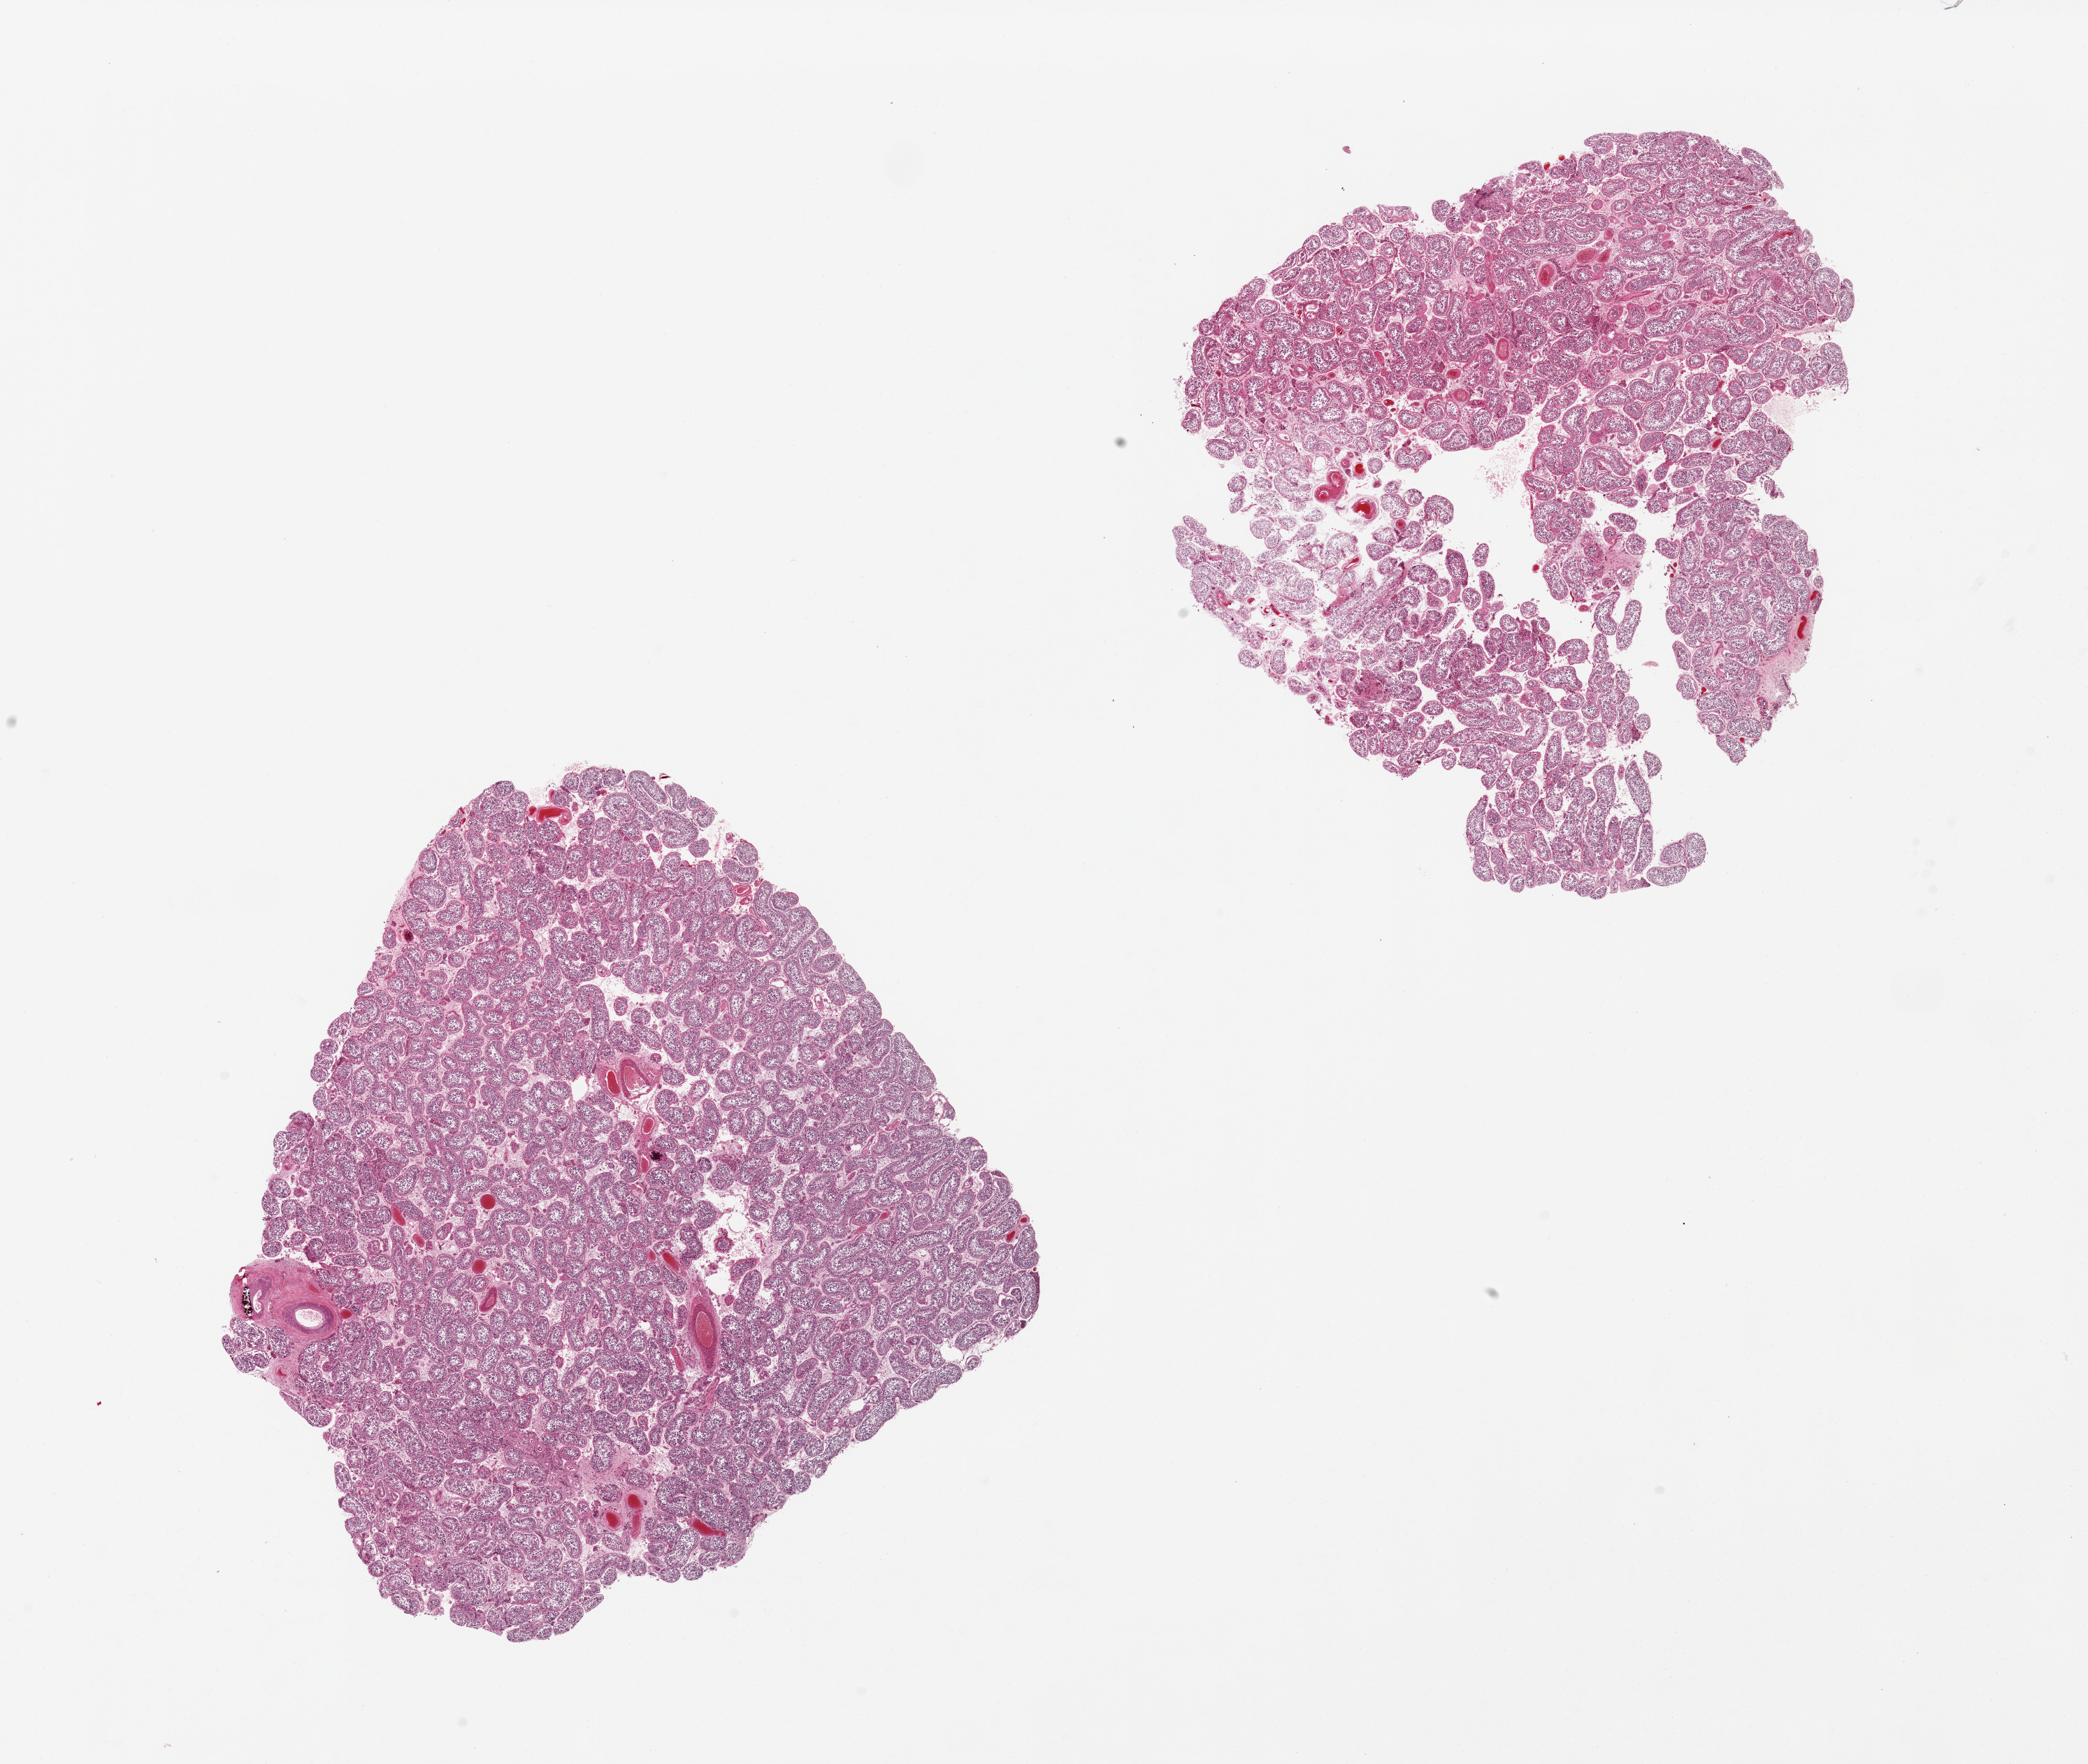
Hematoxylin and eosin (H&E) whole-slide image, brightfield — shown as a low-resolution overview of the whole scanned area (about 23.6 x 20.0 mm, slide scanned at 20x), PAXgene-fixed, paraffin-embedded tissue, target tissue: testis, donor tissue sample. Donor: male.
Reviewer comment on this tissue sample: 2 pieces; spermatogenesis present, medial calcific sclerosis in one vessel.